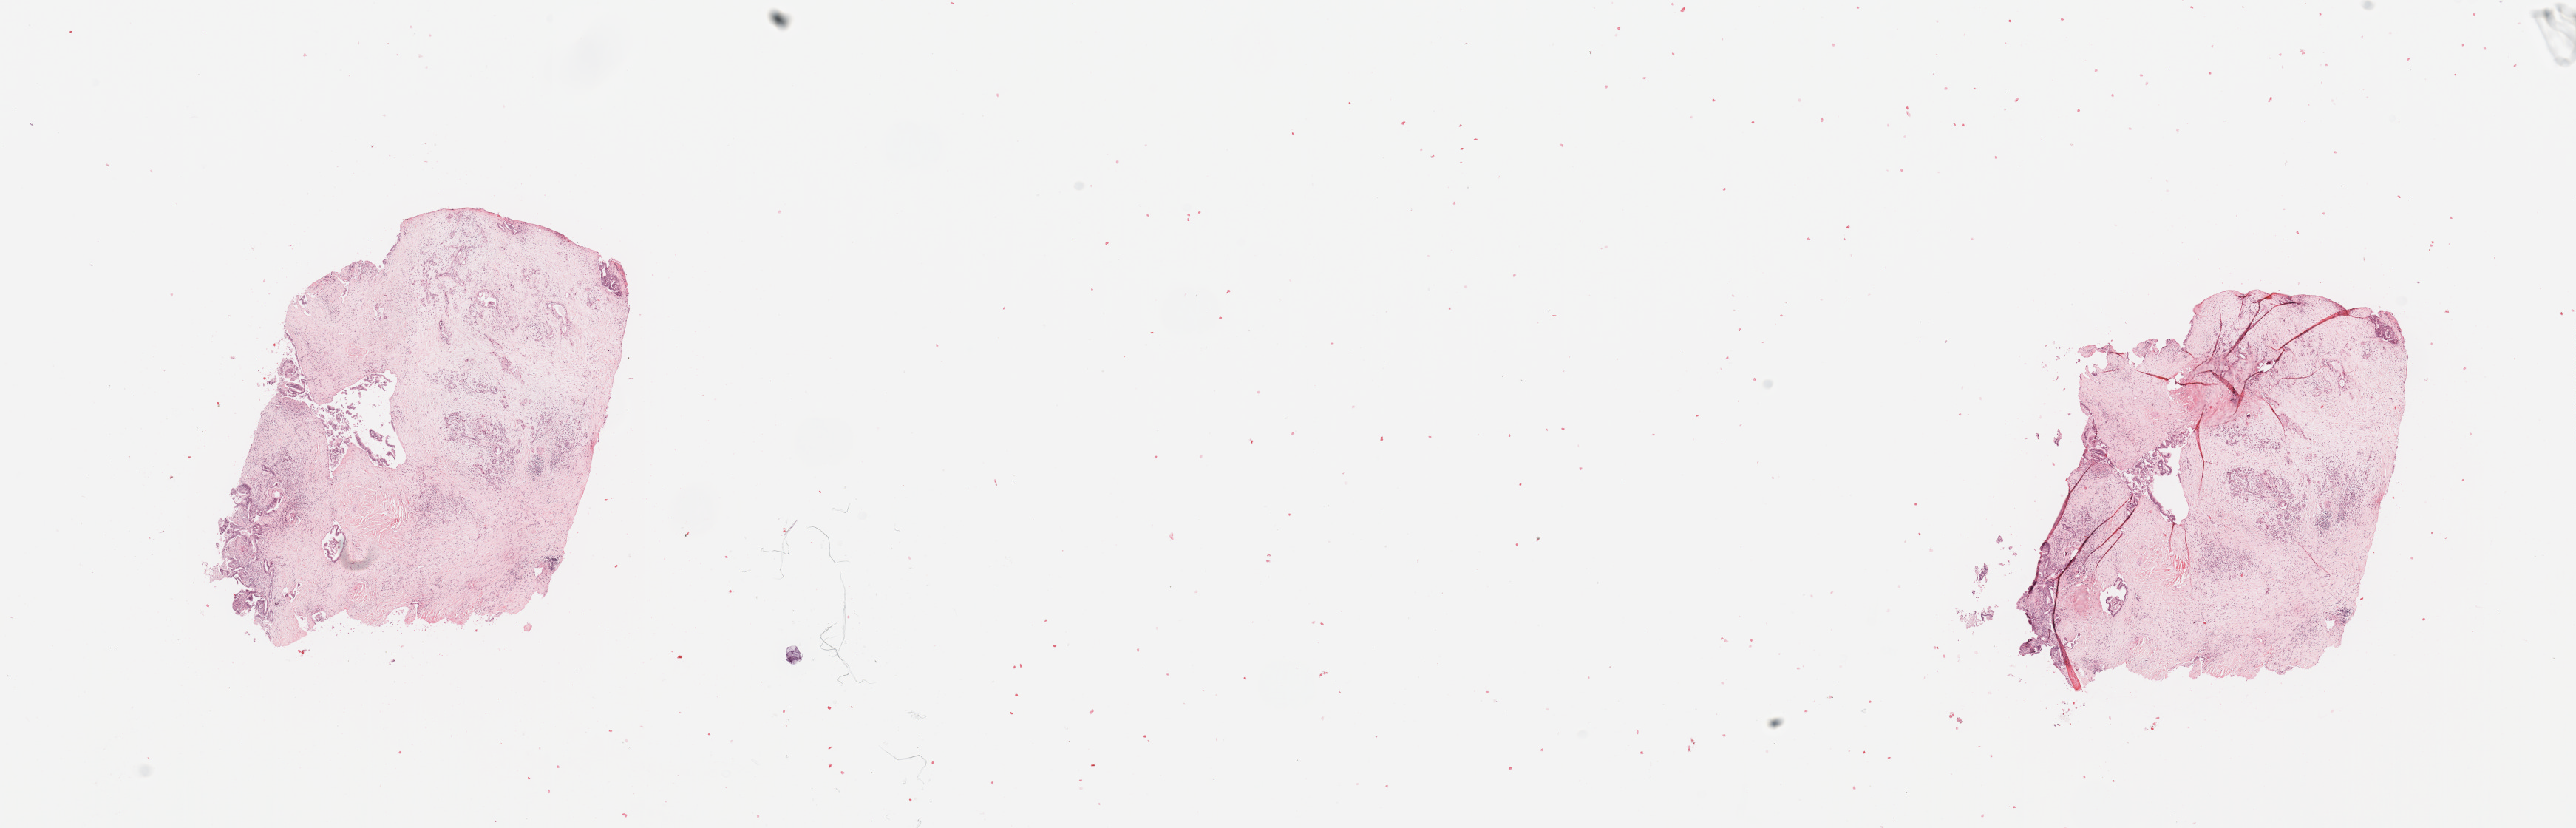
Whole-slide histology image, H&E-stained — low-resolution overview of the scanned area, about 27.6 x 8.9 mm; tumour tissue sample, pancreas. Female, 62 y/o. Histologic grade: G3 (poorly differentiated).
• AJCC pathologic stage: III
• primary tumour site (as recorded): head
• diagnosis: Infiltrating duct carcinoma, NOS